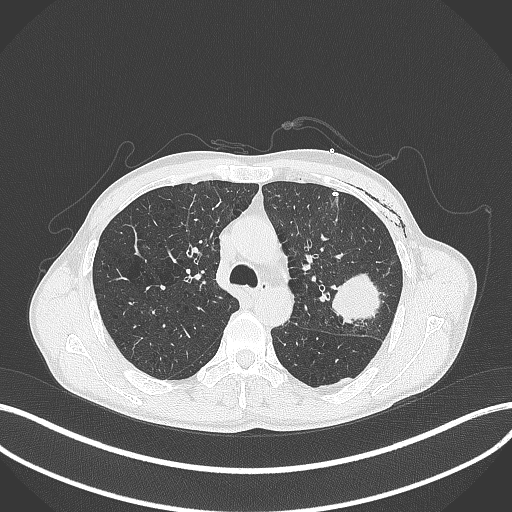
Chest CT, one axial slice; position 275 of 457 along the scan axis; reconstruction kernel B70f; 120 kVp; lung window (W 1500 / L -600 HU); 1 mm slice thickness; 512 × 512 image matrix, field of view 400 × 400 mm. Male patient, age 58 years. From the clinical record (not read from this slice): clinical TNM (as recorded): T3 N0 M0.
Structures marked on this image (rectangle marked by the reading radiologist):
- lung tumour (recorded histology: adenocarcinoma): bounding box (x1, y1, x2, y2) in pixels: (330, 270, 389, 326)